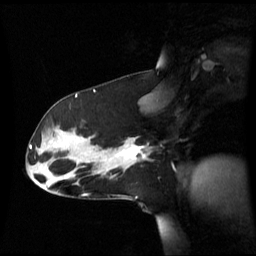
Breast MRI (dynamic contrast-enhanced), one sagittal slice; position 37 of 60 along the scan axis; dynamic contrast-enhanced series, image 2 of 3 at this slice position (ordered by acquisition); 1.5 T; TE 4.2 ms, TR 8.4 ms; 2.8 mm slice thickness; 256 × 256 image matrix, field of view 270 × 270 mm. Patient: female, 39 years. Case-level facts recorded for this patient, not image findings: setting: breast cancer imaged before/during neoadjuvant chemotherapy; receptor status: triple-negative.
Structures marked on this image (semi-automatically segmented with operator editing):
- analysis volume of interest (the breast-tissue region the enhancement analysis was run in; not a lesion): bounding box (x1, y1, x2, y2) in pixels: (101, 137, 151, 173)
- tumour enhancement mask (voxels above the 70 % enhancement threshold inside the analysis volume of interest): (120, 144, 146, 160)